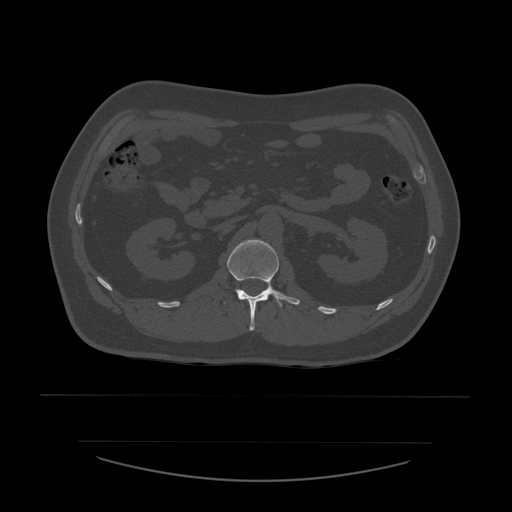
CT including the spine, one axial slice. Slice 223 of 532 in the series (ordered by position). Bone window (W 1800 / L 400 HU). 1.25 mm slice thickness. 512 × 512 image matrix, field of view 441 × 441 mm. Patient age 44 years. Case-level facts recorded for this patient, not image findings: primary cancer: soft tissue sarcoma.
Annotated regions visible in this slice (semi-automatically segmented with operator editing):
- L1 vertebra: box from (x=224, y=239) to (x=301, y=331) px